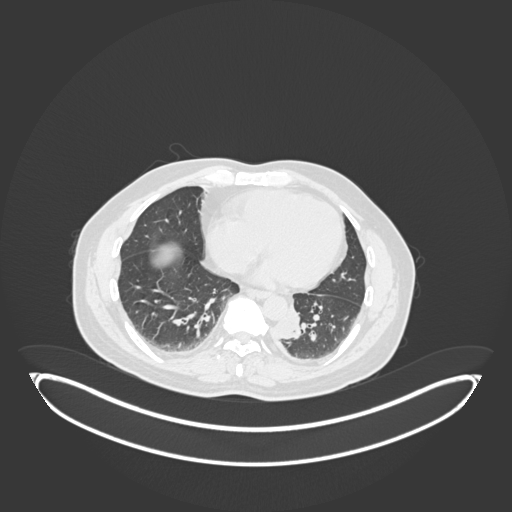
Chest CT, one axial slice. Slice 59 of 258 in the series (ordered by position). Reconstruction kernel B30f. 120 kVp. Lung window (W 1500 / L -600 HU). 1 mm slice thickness. 512 × 512 image matrix, field of view 500 × 500 mm. Male patient, age 54 years. Case-level facts recorded for this patient, not image findings: clinical TNM (as recorded): T3 N0 M0.
Annotated regions visible in this slice (rectangle marked by the reading radiologist):
- lung tumour (recorded histology: squamous cell carcinoma): bounding box [x1, y1, x2, y2] px = [275, 309, 302, 341]